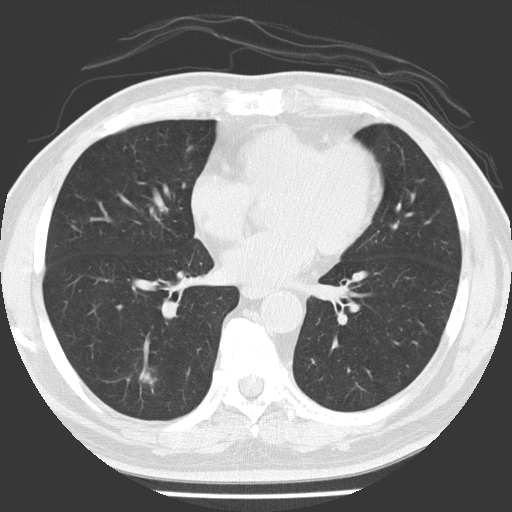
Chest CT (low-dose screening protocol), one axial image; baseline screening round; lung window (W 1500 / L -600 HU); 2 mm slice thickness; lung (sharp) reconstruction kernel (FC51); 120 kVp; slice 86 of 154 in the series. Male, age 56 years at enrolment.
• Lesion marked by an expert reader, bounding box [x1, y1, x2, y2] px = [119, 355, 170, 404].
• The exam's reader record, not a measurement of the box and not confirmed to be the same lesion: non-calcified nodule or mass ≥4 mm, right lower lobe, 21 × 17 mm, spiculated (stellate) margins, soft tissue attenuation.
• Official screen result: positive, change unspecified: nodule(s) >= 4 mm or enlarging nodule(s), mass(es), or other non-specific abnormalities suspicious for lung cancer.